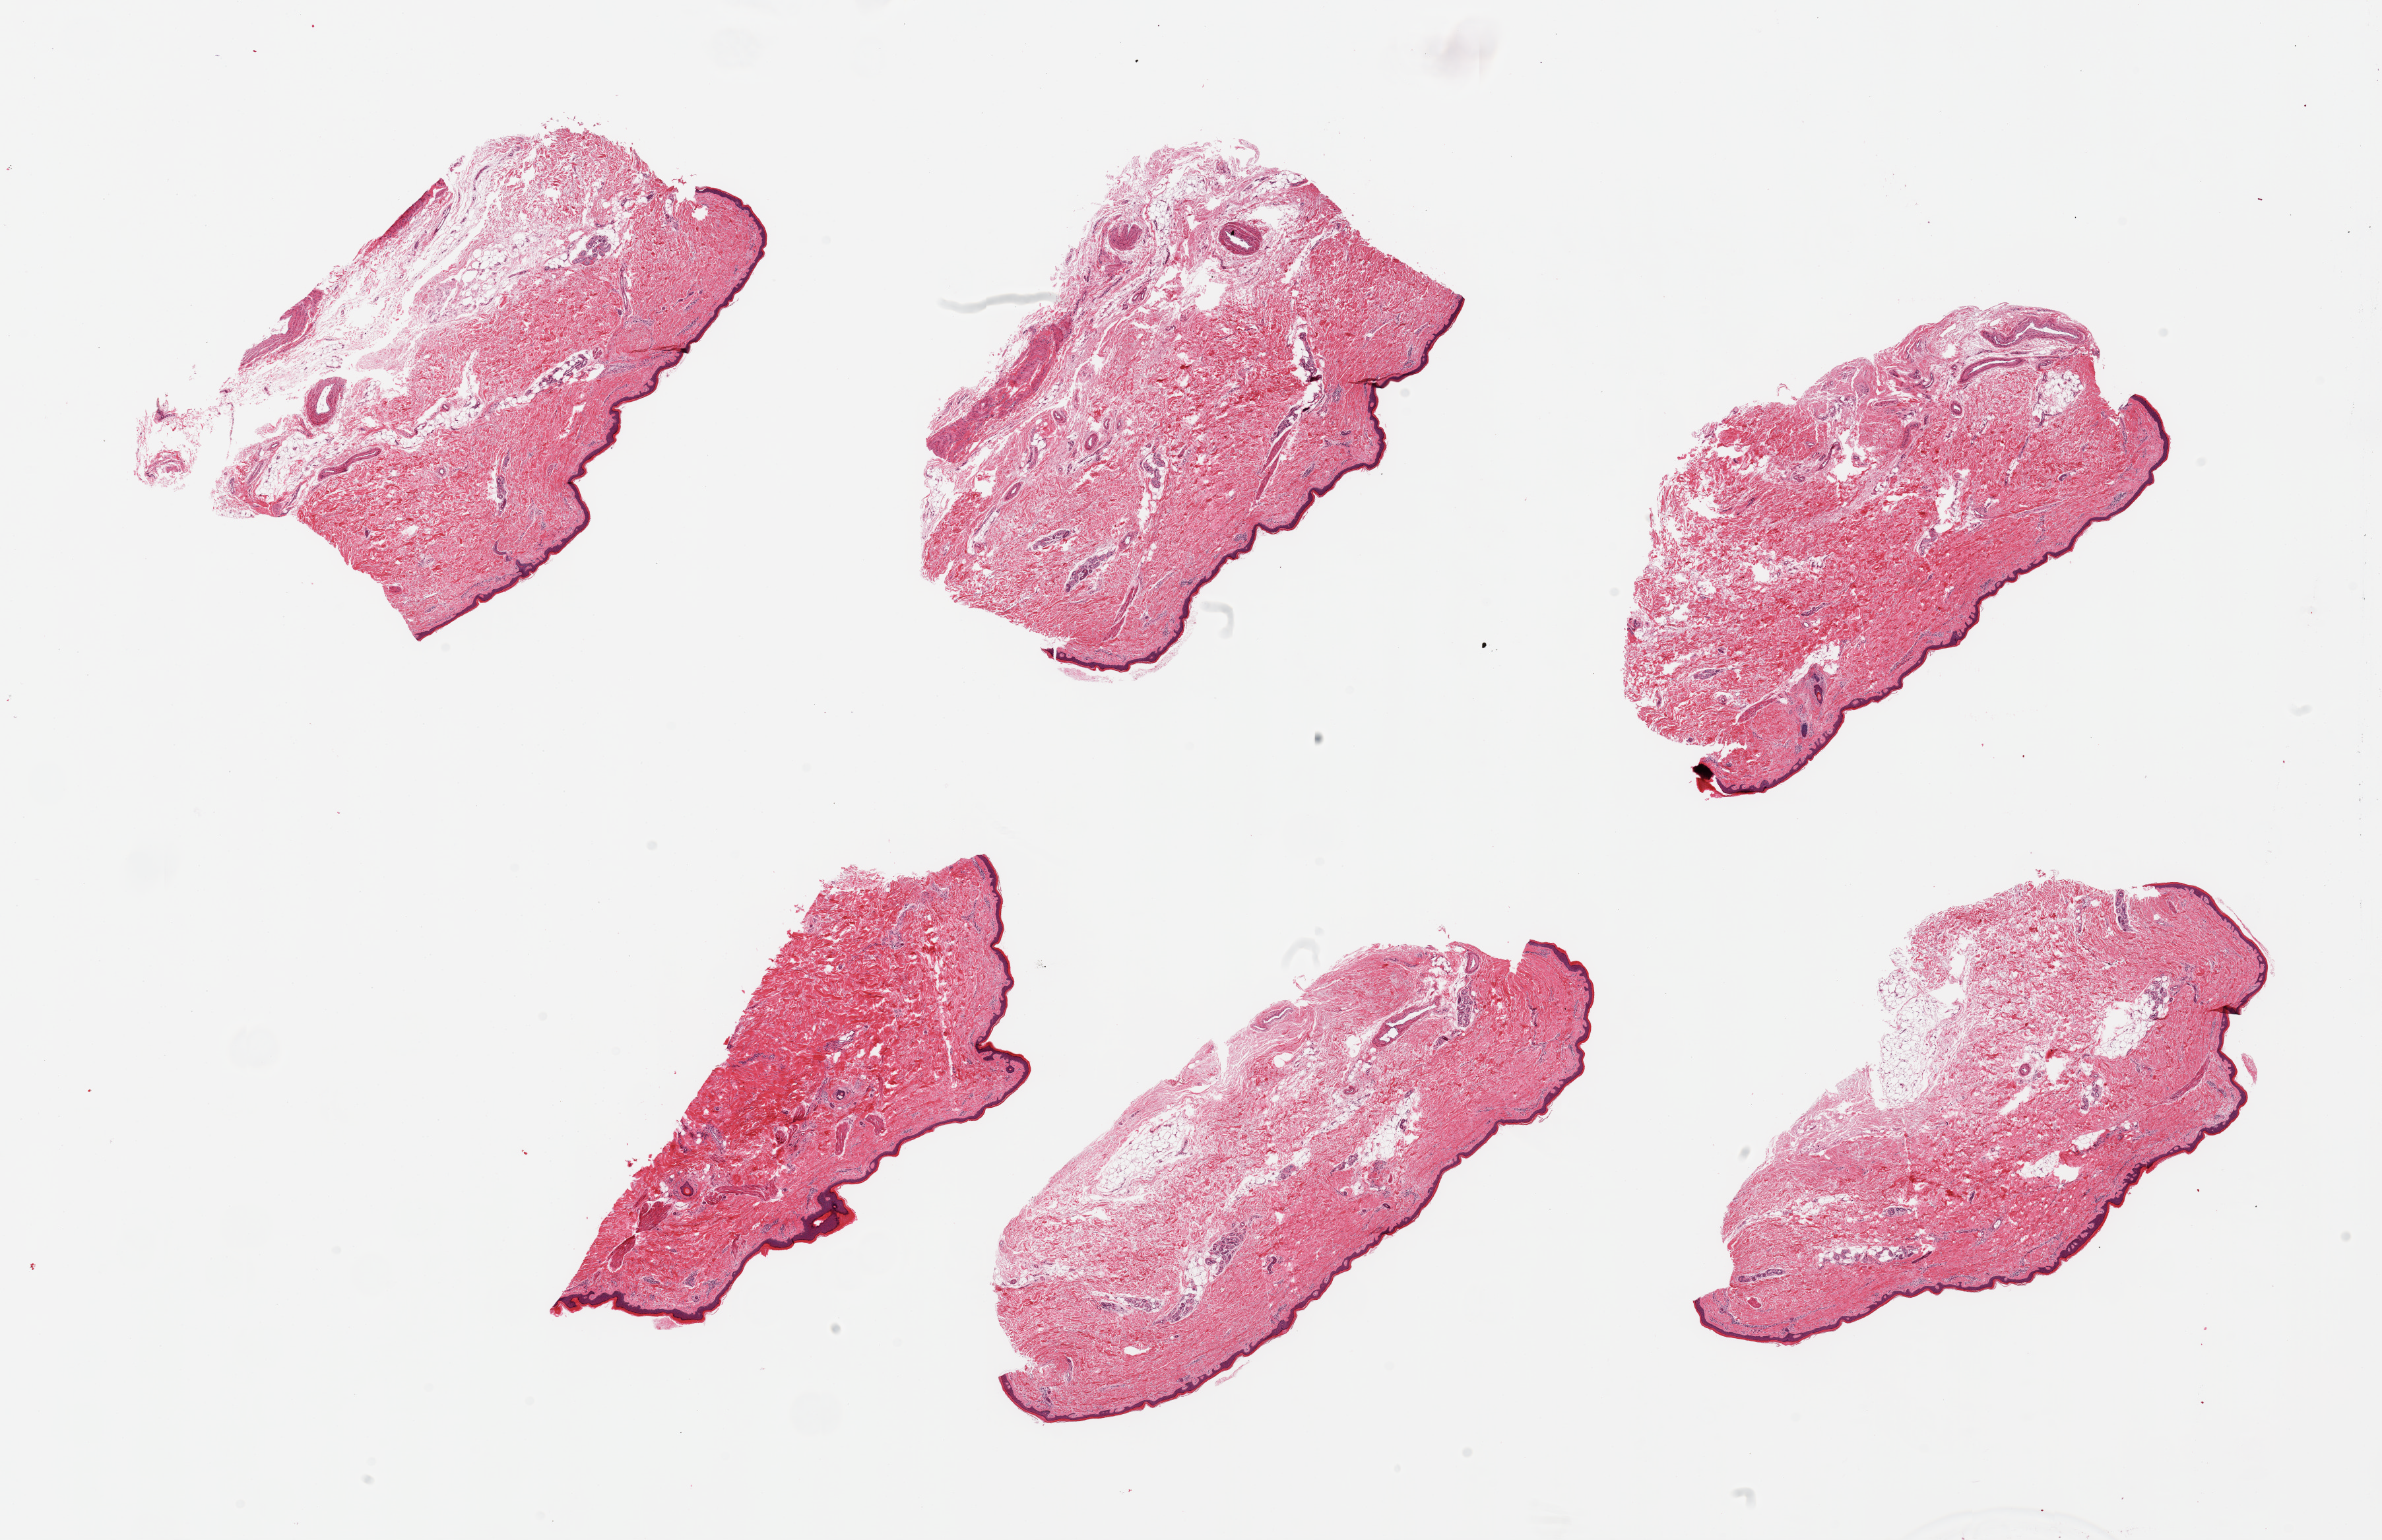
Digitized hematoxylin and eosin (H&E)-stained section — whole scanned area (about 28.5 x 18.5 mm, acquisition: 20x scan) shown as a low-resolution overview. PAXgene-fixed, paraffin-embedded tissue. Sampled site (target tissue): skin of lower leg. Tissue donor sample. Male donor.
Review note (as recorded): 6 pieces, adherent fat up to ~1mm; squamous epithelium ~50 microns.